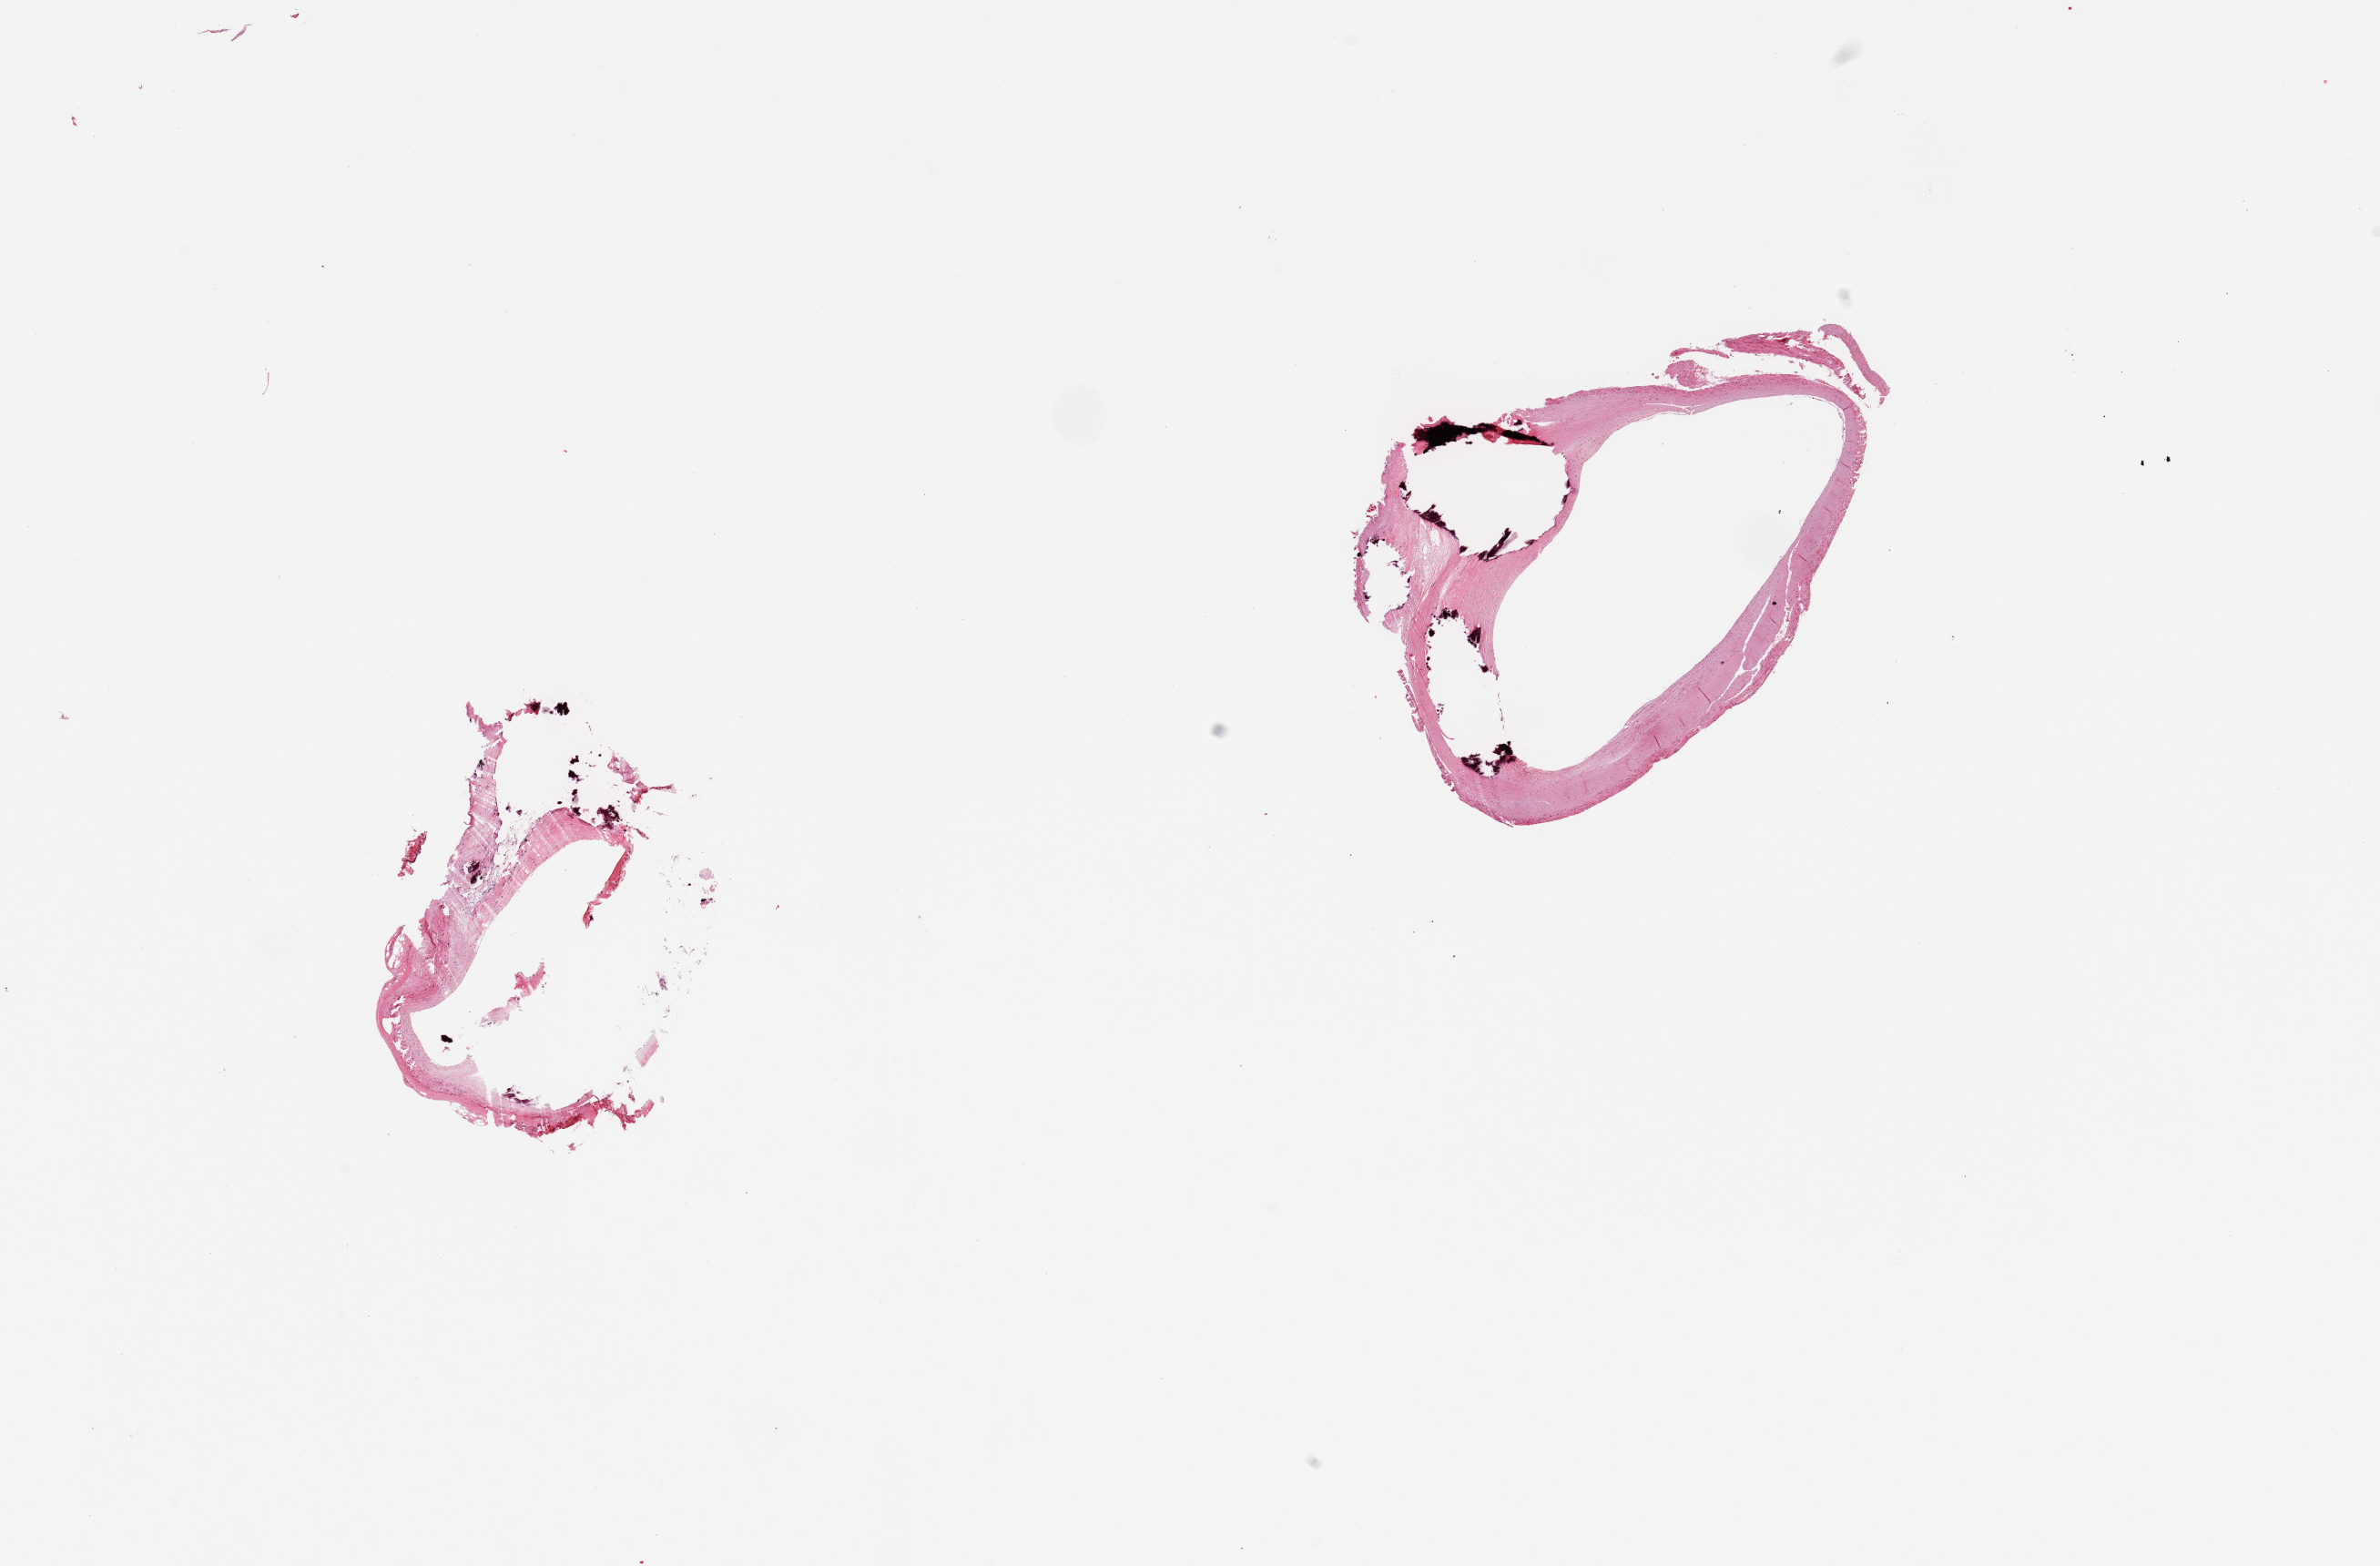
Haematoxylin and eosin whole-slide image — shown as a low-resolution overview of the whole scanned area (about 20.7 x 13.6 mm), PAXgene-fixed paraffin-embedded (PFPE) section, sampled site (target tissue): coronary artery, donor tissue sample.
• review note (as recorded): 2 pieces, focally ~30% occlusive calcifed atherosis